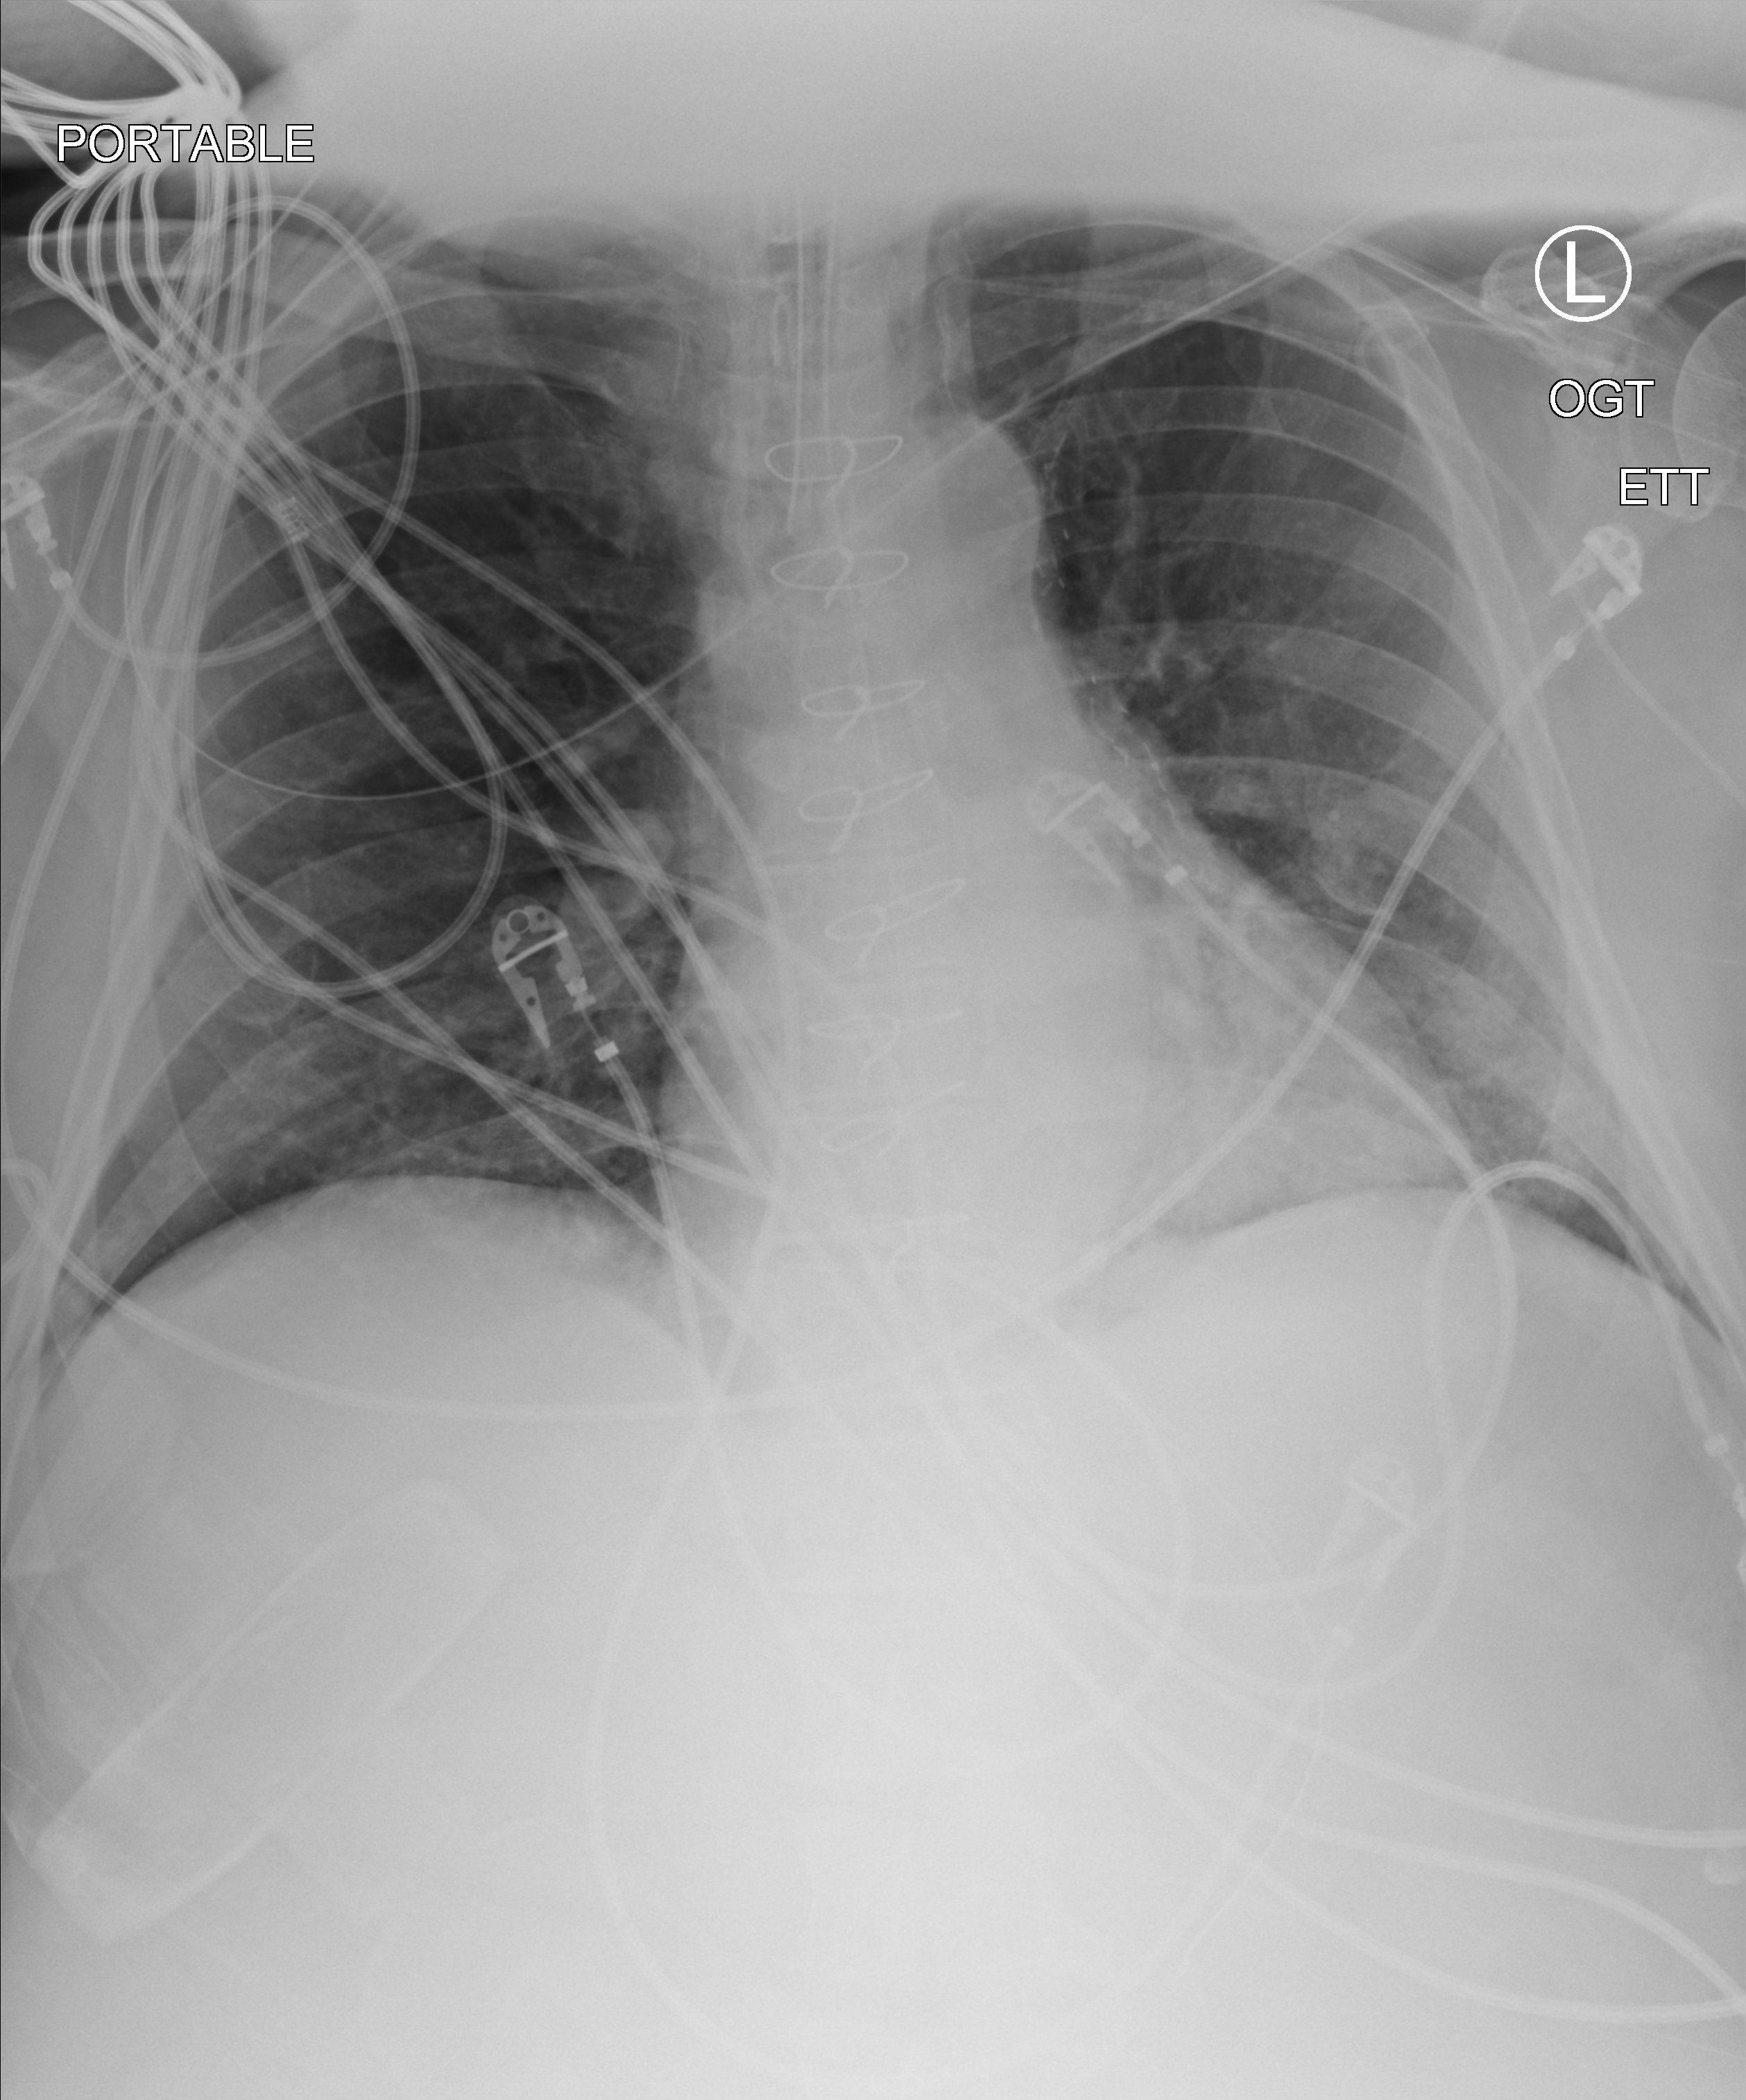
Bedside chest radiograph (computed radiography). Male patient hospitalised with COVID-19, age 60–74 years.
Hospital-stay facts (about this admission, not read from this image; timing relative to this image not recorded):
- admitted to intensive care during this hospital stay: yes